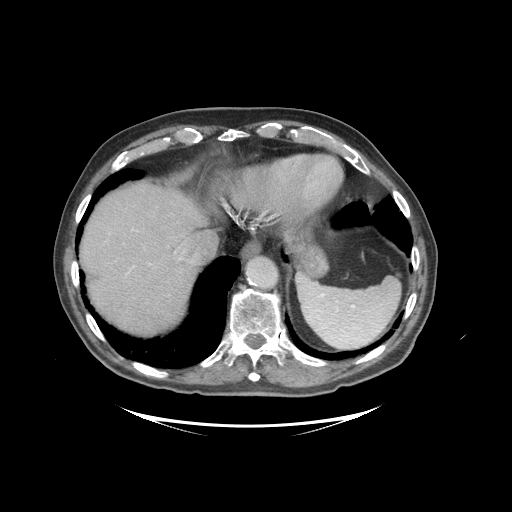
Contrast-enhanced abdominal CT (liver protocol), one axial slice; position 82 of 99 along the scan axis; soft-tissue window (W 400 / L 40 HU); 512 × 512 image matrix, field of view 460 × 460 mm. Case-level facts recorded for this patient, not image findings: diagnosis: hepatocellular carcinoma (patient treated with transarterial chemoembolisation; whether this scan precedes or follows treatment is not stated here); TNM stage (as recorded): Stage-I; Child-Pugh class: A; tumour differentiation: moderately differentiated; tumour nodularity: uninodular.
Outlined on this slice (semi-automatically segmented with operator editing):
- liver parenchyma outside the tumour (the mass and vessels are separate outlines, so this box may not span the whole liver): bounding box (x1, y1, x2, y2) in pixels: (80, 184, 218, 334)
- liver vessels: (128, 229, 182, 273)